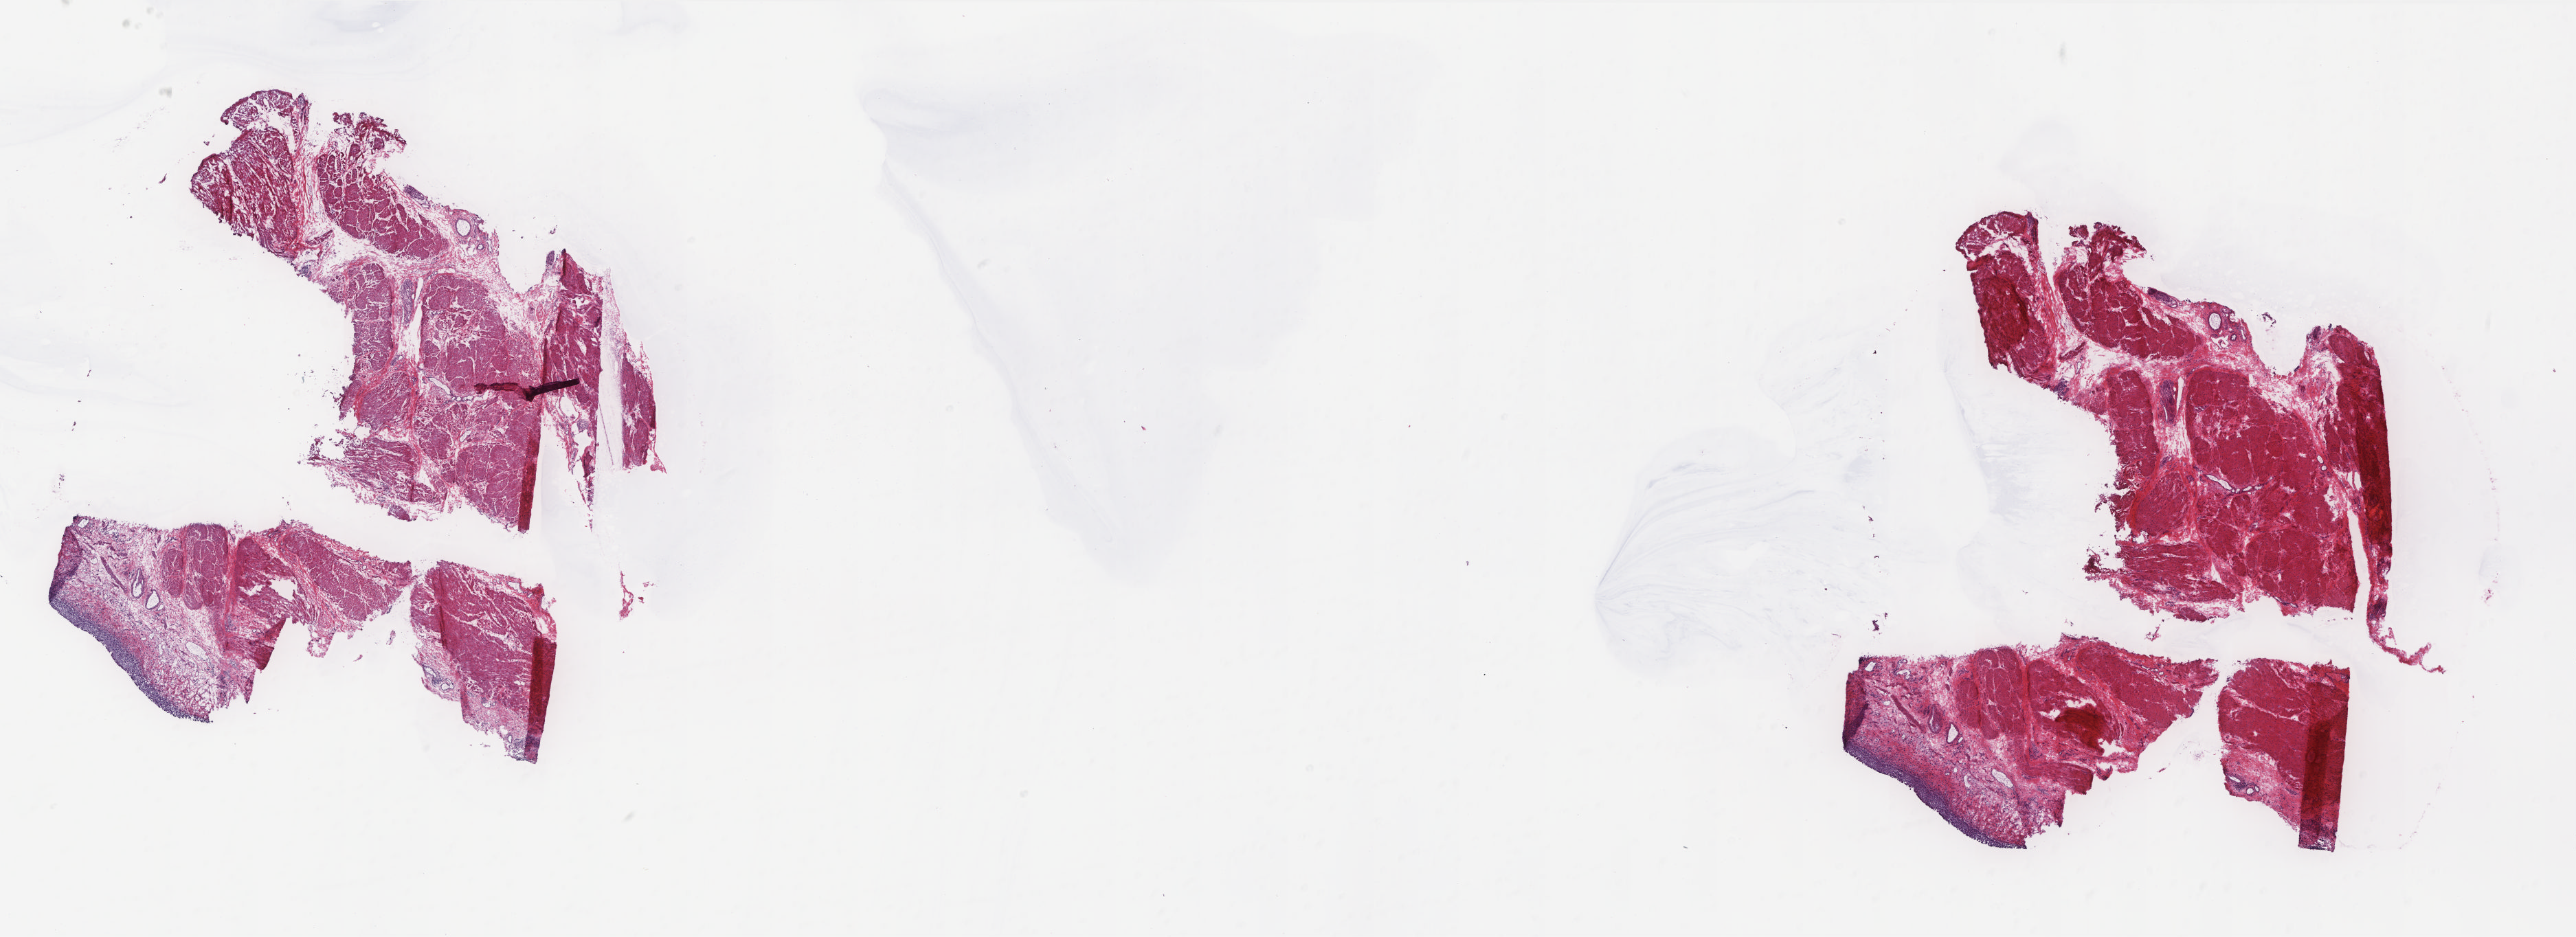
Whole-slide histology image, Hematoxylin and eosin (H&E) stained — shown as a low-resolution overview of the whole scanned area (about 29.9 x 10.9 mm, acquisition: 20x scan); frozen section from the top of the tissue portion; solid tissue normal (non-tumour tissue) sample from the bladder. Female patient; age at initial diagnosis 57 years. Pathologist review of this section (percent, as recorded): tumour cells 0%, tumour nuclei 0%, normal cells 3%, stromal cells 97%, necrosis 0%. Inflammatory infiltration, as recorded: lymphocyte infiltration 2%, monocyte infiltration 0%, neutrophil infiltration 0%.
* this section: solid tissue normal sample (biorepository sample class)
* patient diagnosis: Transitional cell carcinoma